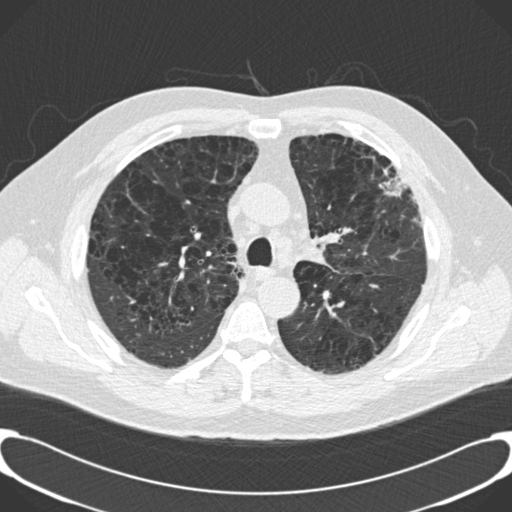
Low-dose screening chest CT, axial slice; third annual screen; lung window (W 1500 / L -600 HU); 120 kVp; slice 51 of 189 in the series. Male, age 59 years at enrolment.
- Expert-annotated lung lesion, bounding box <357,147,420,221> (left, top, right, bottom; pixels).
- No non-calcified nodule or mass ≥4 mm was recorded by the screening reader at this exam.
- Official screen result: positive, other.
- Participant outcome: lung cancer diagnosed 134 days after this screen — bronchiolo-alveolar carcinoma, mixed mucinous and non-mucinous, left upper lobe, stage IA (AJCC 6th edition), 20 mm at pathology.